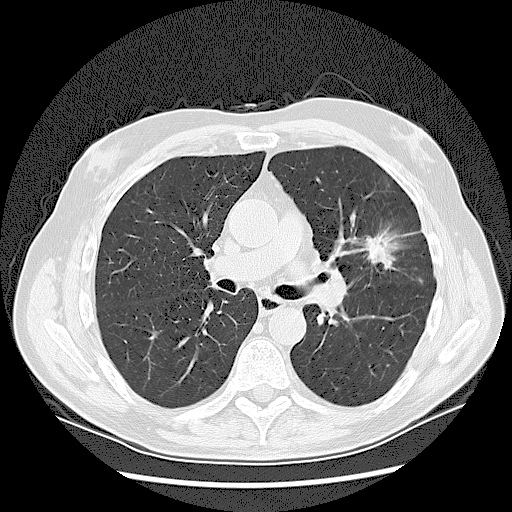
Low-dose screening chest CT, one axial slice; position 77 of 132 along the scan axis; reconstruction kernel LUNG; lung window (W 1500 / L -600 HU); 512 × 512 image matrix, field of view 380 × 380 mm.
Outlined on this slice (outlined manually by an expert reader):
- lesion 1 (tumor, upper lobe of left lung): bounding box <367,237,392,264> (left, top, right, bottom; pixels)